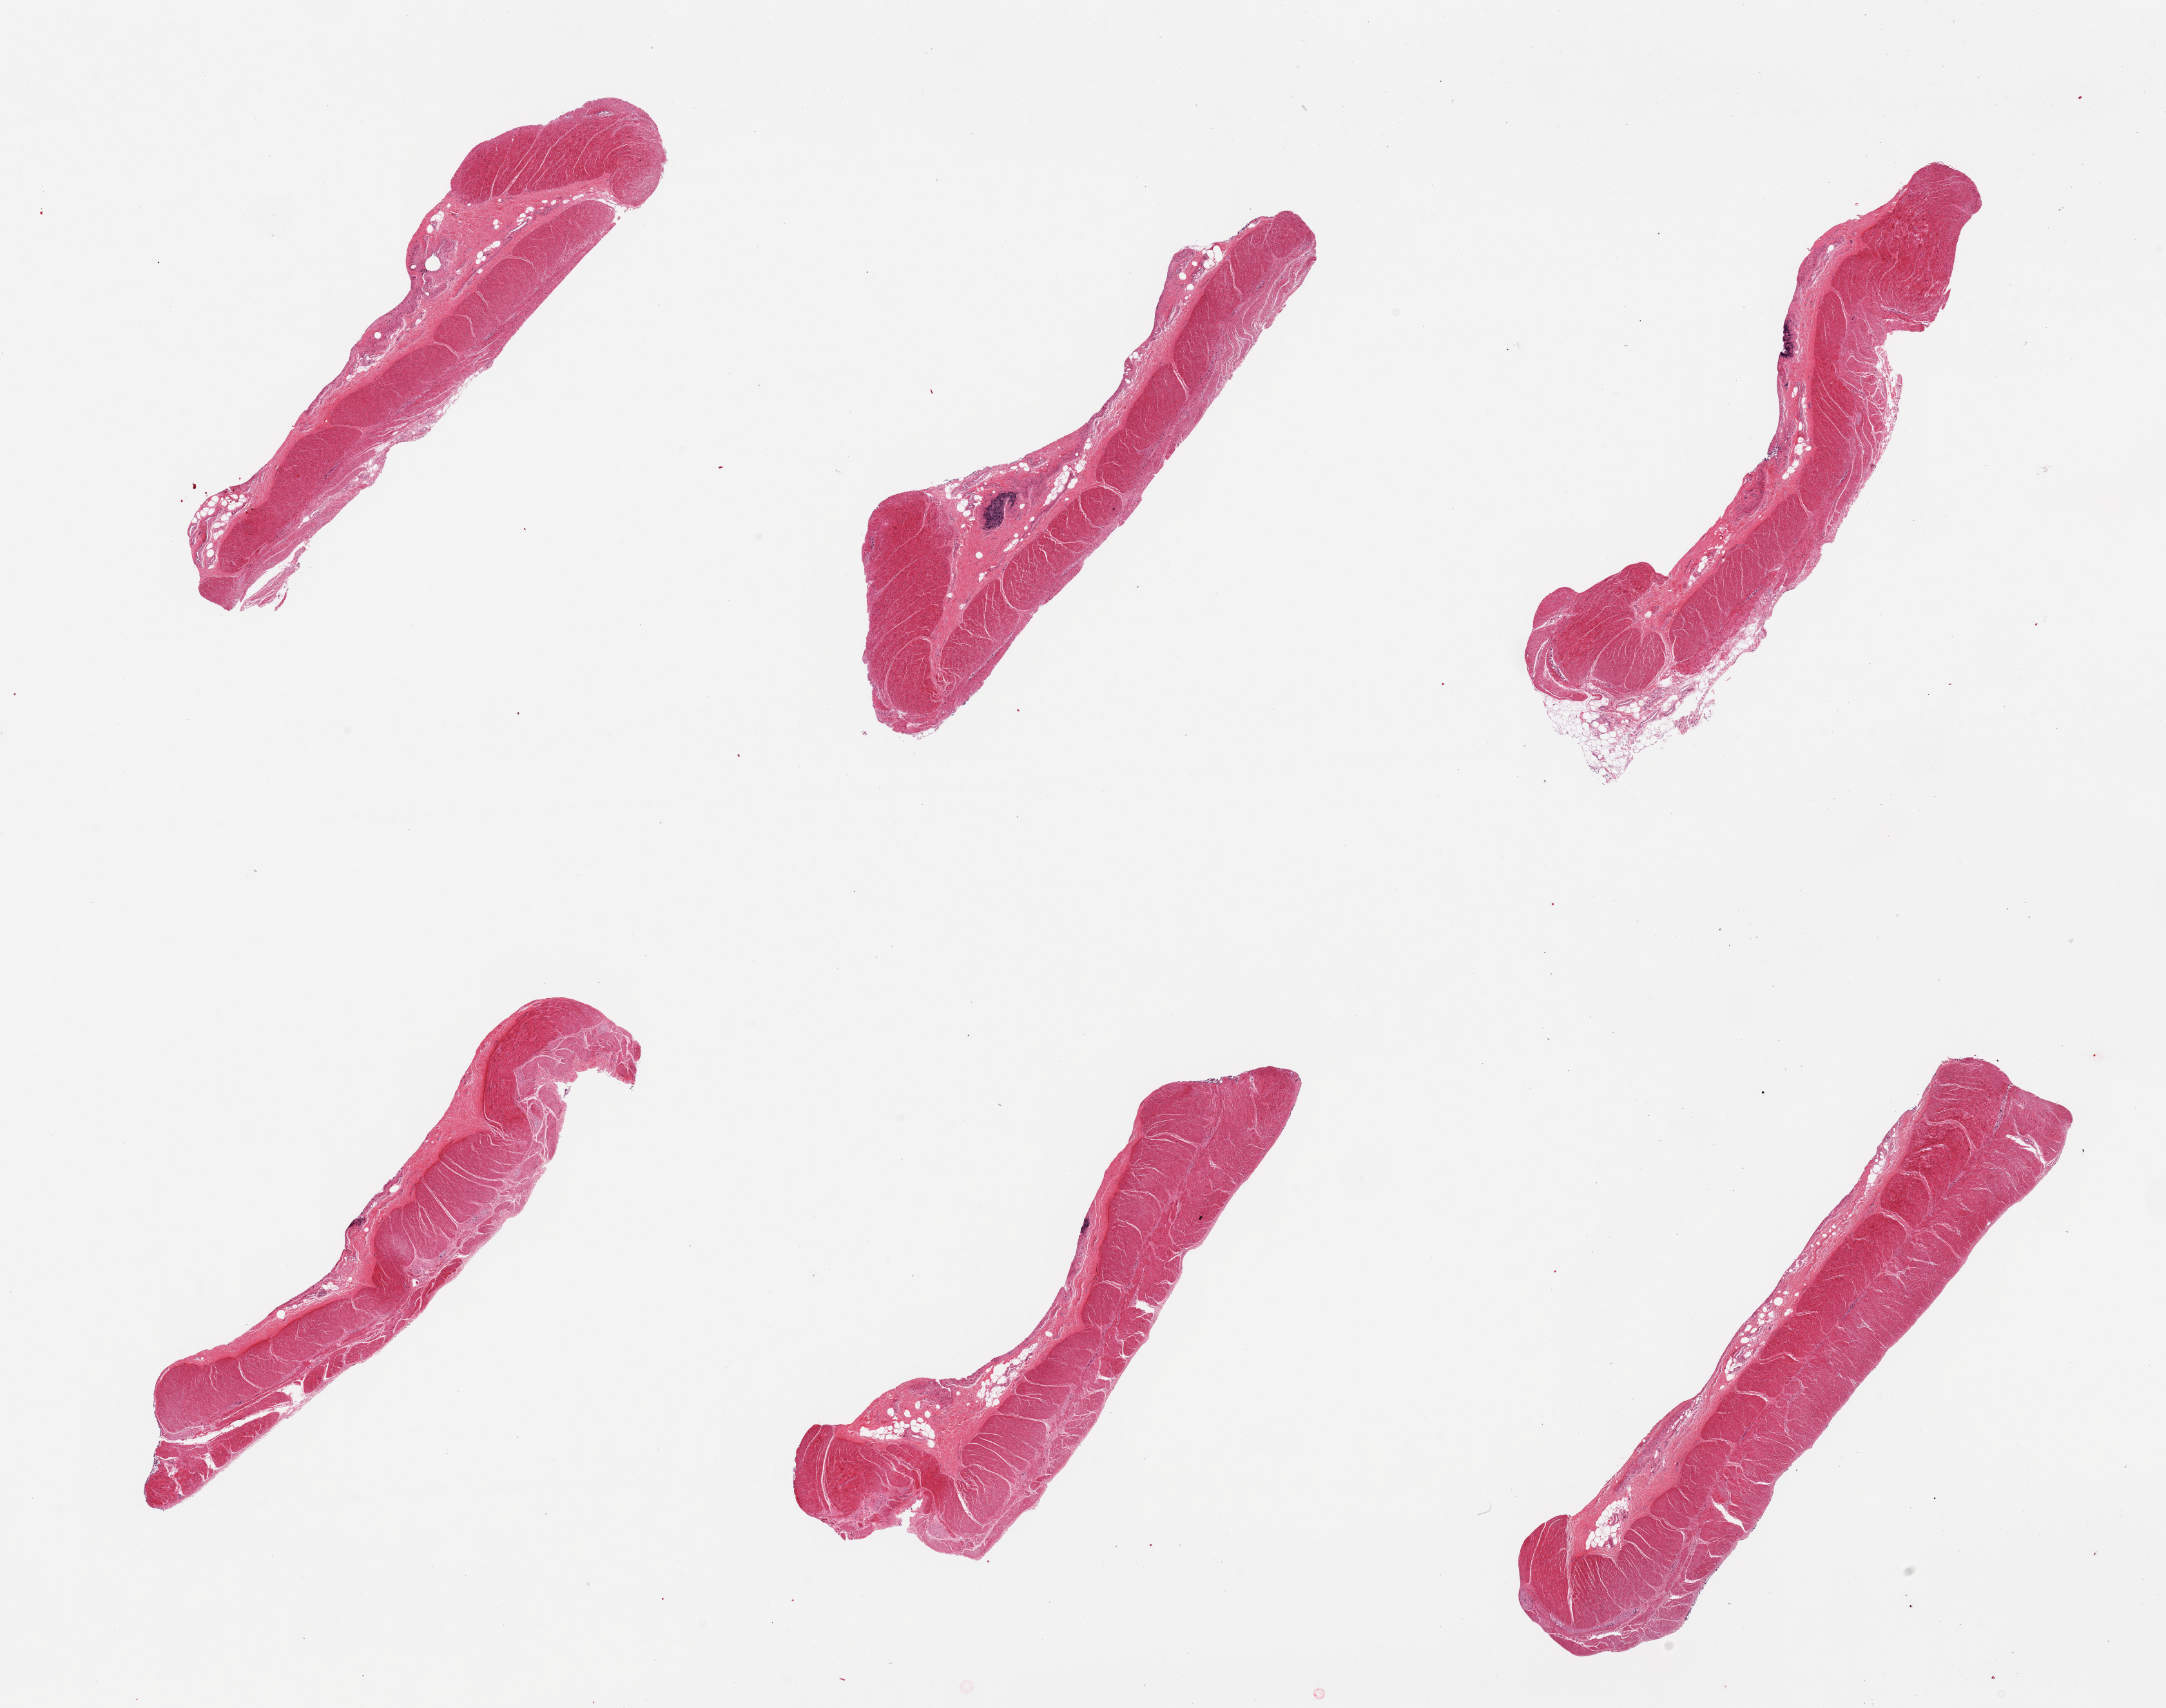
H&E whole-slide image, shown as a low-resolution overview of the whole scanned area (about 26.6 x 21.0 mm, slide scanned at 20x); PAXgene-fixed paraffin-embedded (PFPE) section; section of sigmoid colon (target tissue); donor tissue sample.
Review note (as recorded): 6 pieces. well dissected muscularis propria.